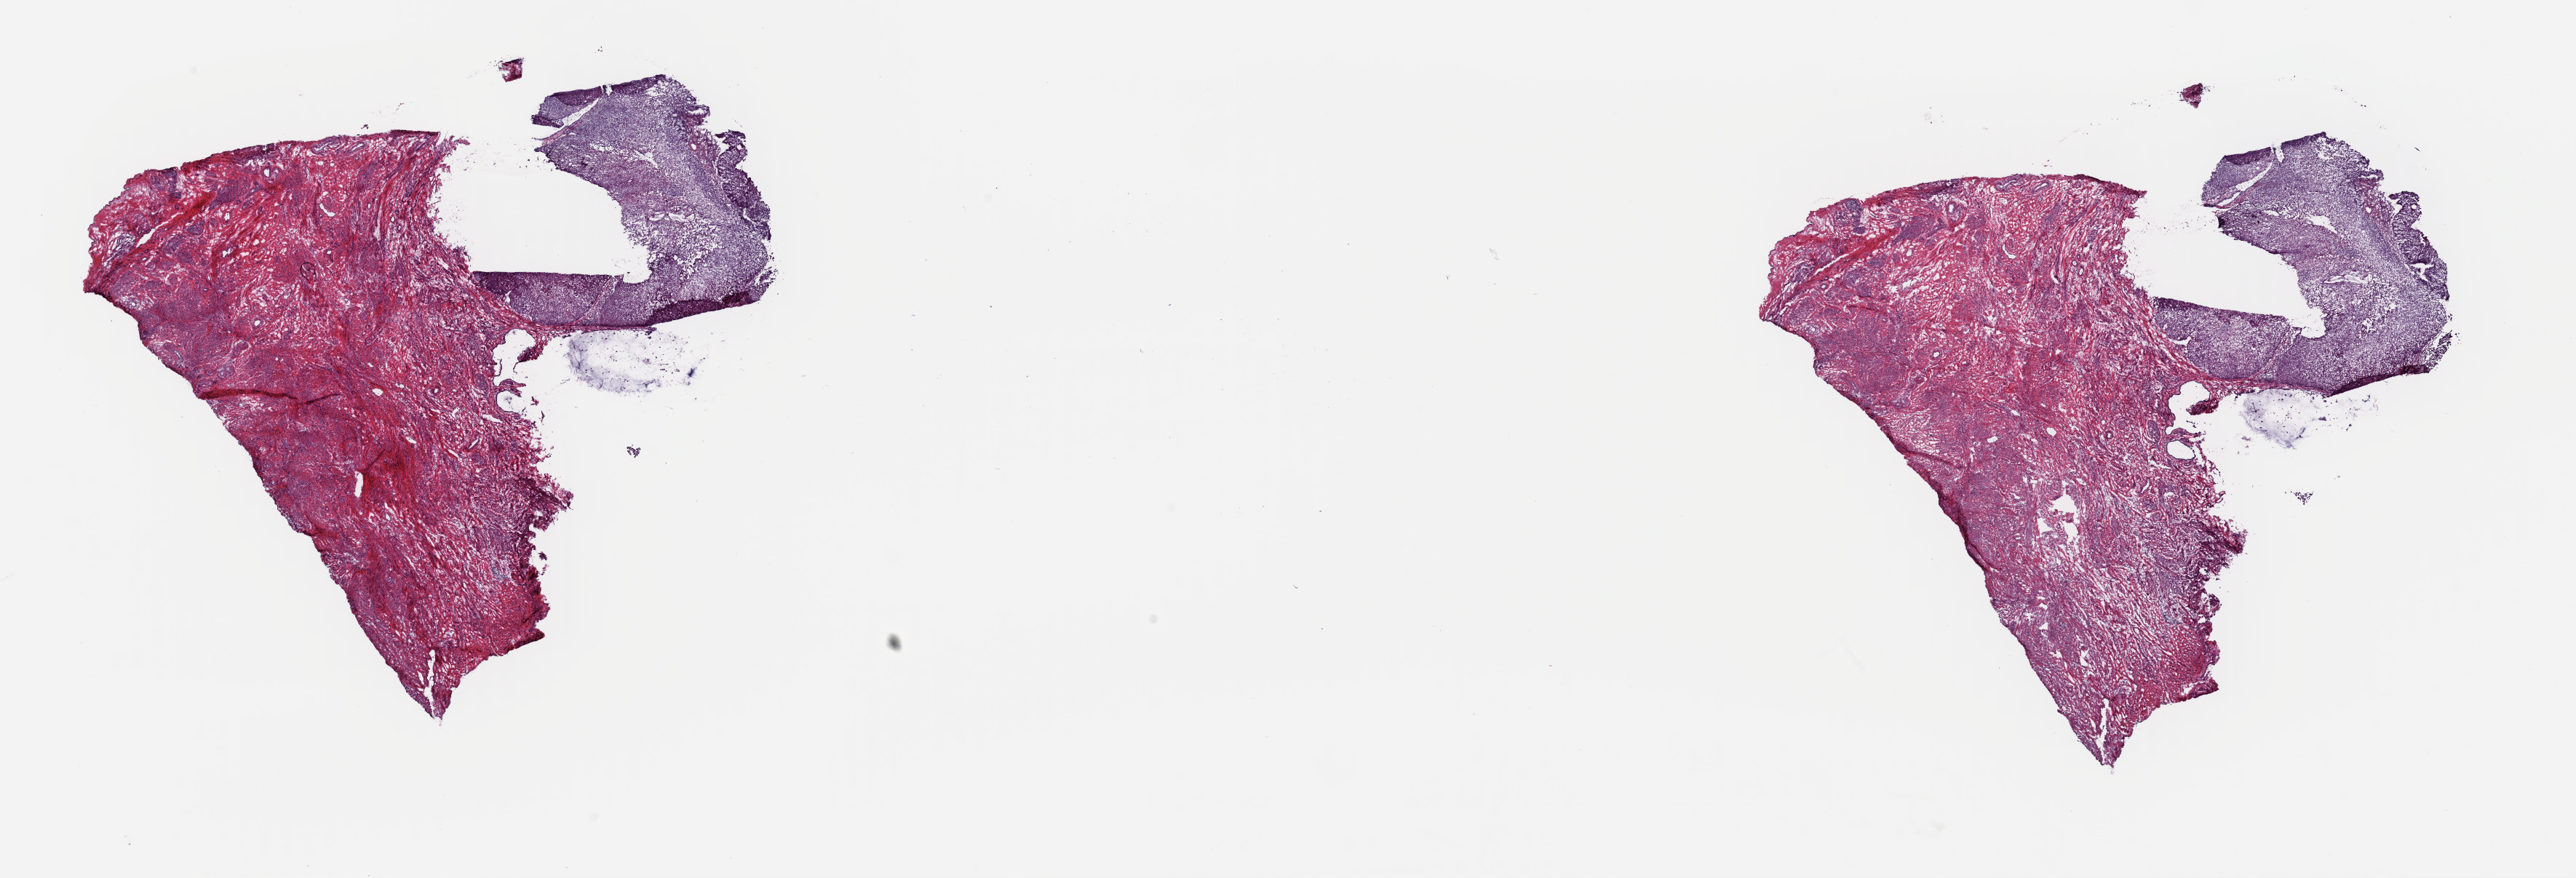
Hematoxylin and eosin (H&E) stained whole-slide image, shown as a low-resolution overview of the whole scanned area (about 28.0 x 9.5 mm, from a 40x scan), frozen section, primary tumour sample from the cervix. Patient: female, age at initial diagnosis 57 years. Histologic grade: G2 (moderately differentiated). Composition of this section per pathologist review: tumour cells 65%, tumour nuclei 75%, normal cells 20%, stromal cells 5%, necrosis 10%. Infiltration values recorded for this section: lymphocyte infiltration 1%, monocyte infiltration 1%, neutrophil infiltration 0%.
Diagnosis: Squamous cell carcinoma, NOS (cervix uteri). FIGO stage: II. Lymph nodes positive (case pathology): 0 of 11 examined.